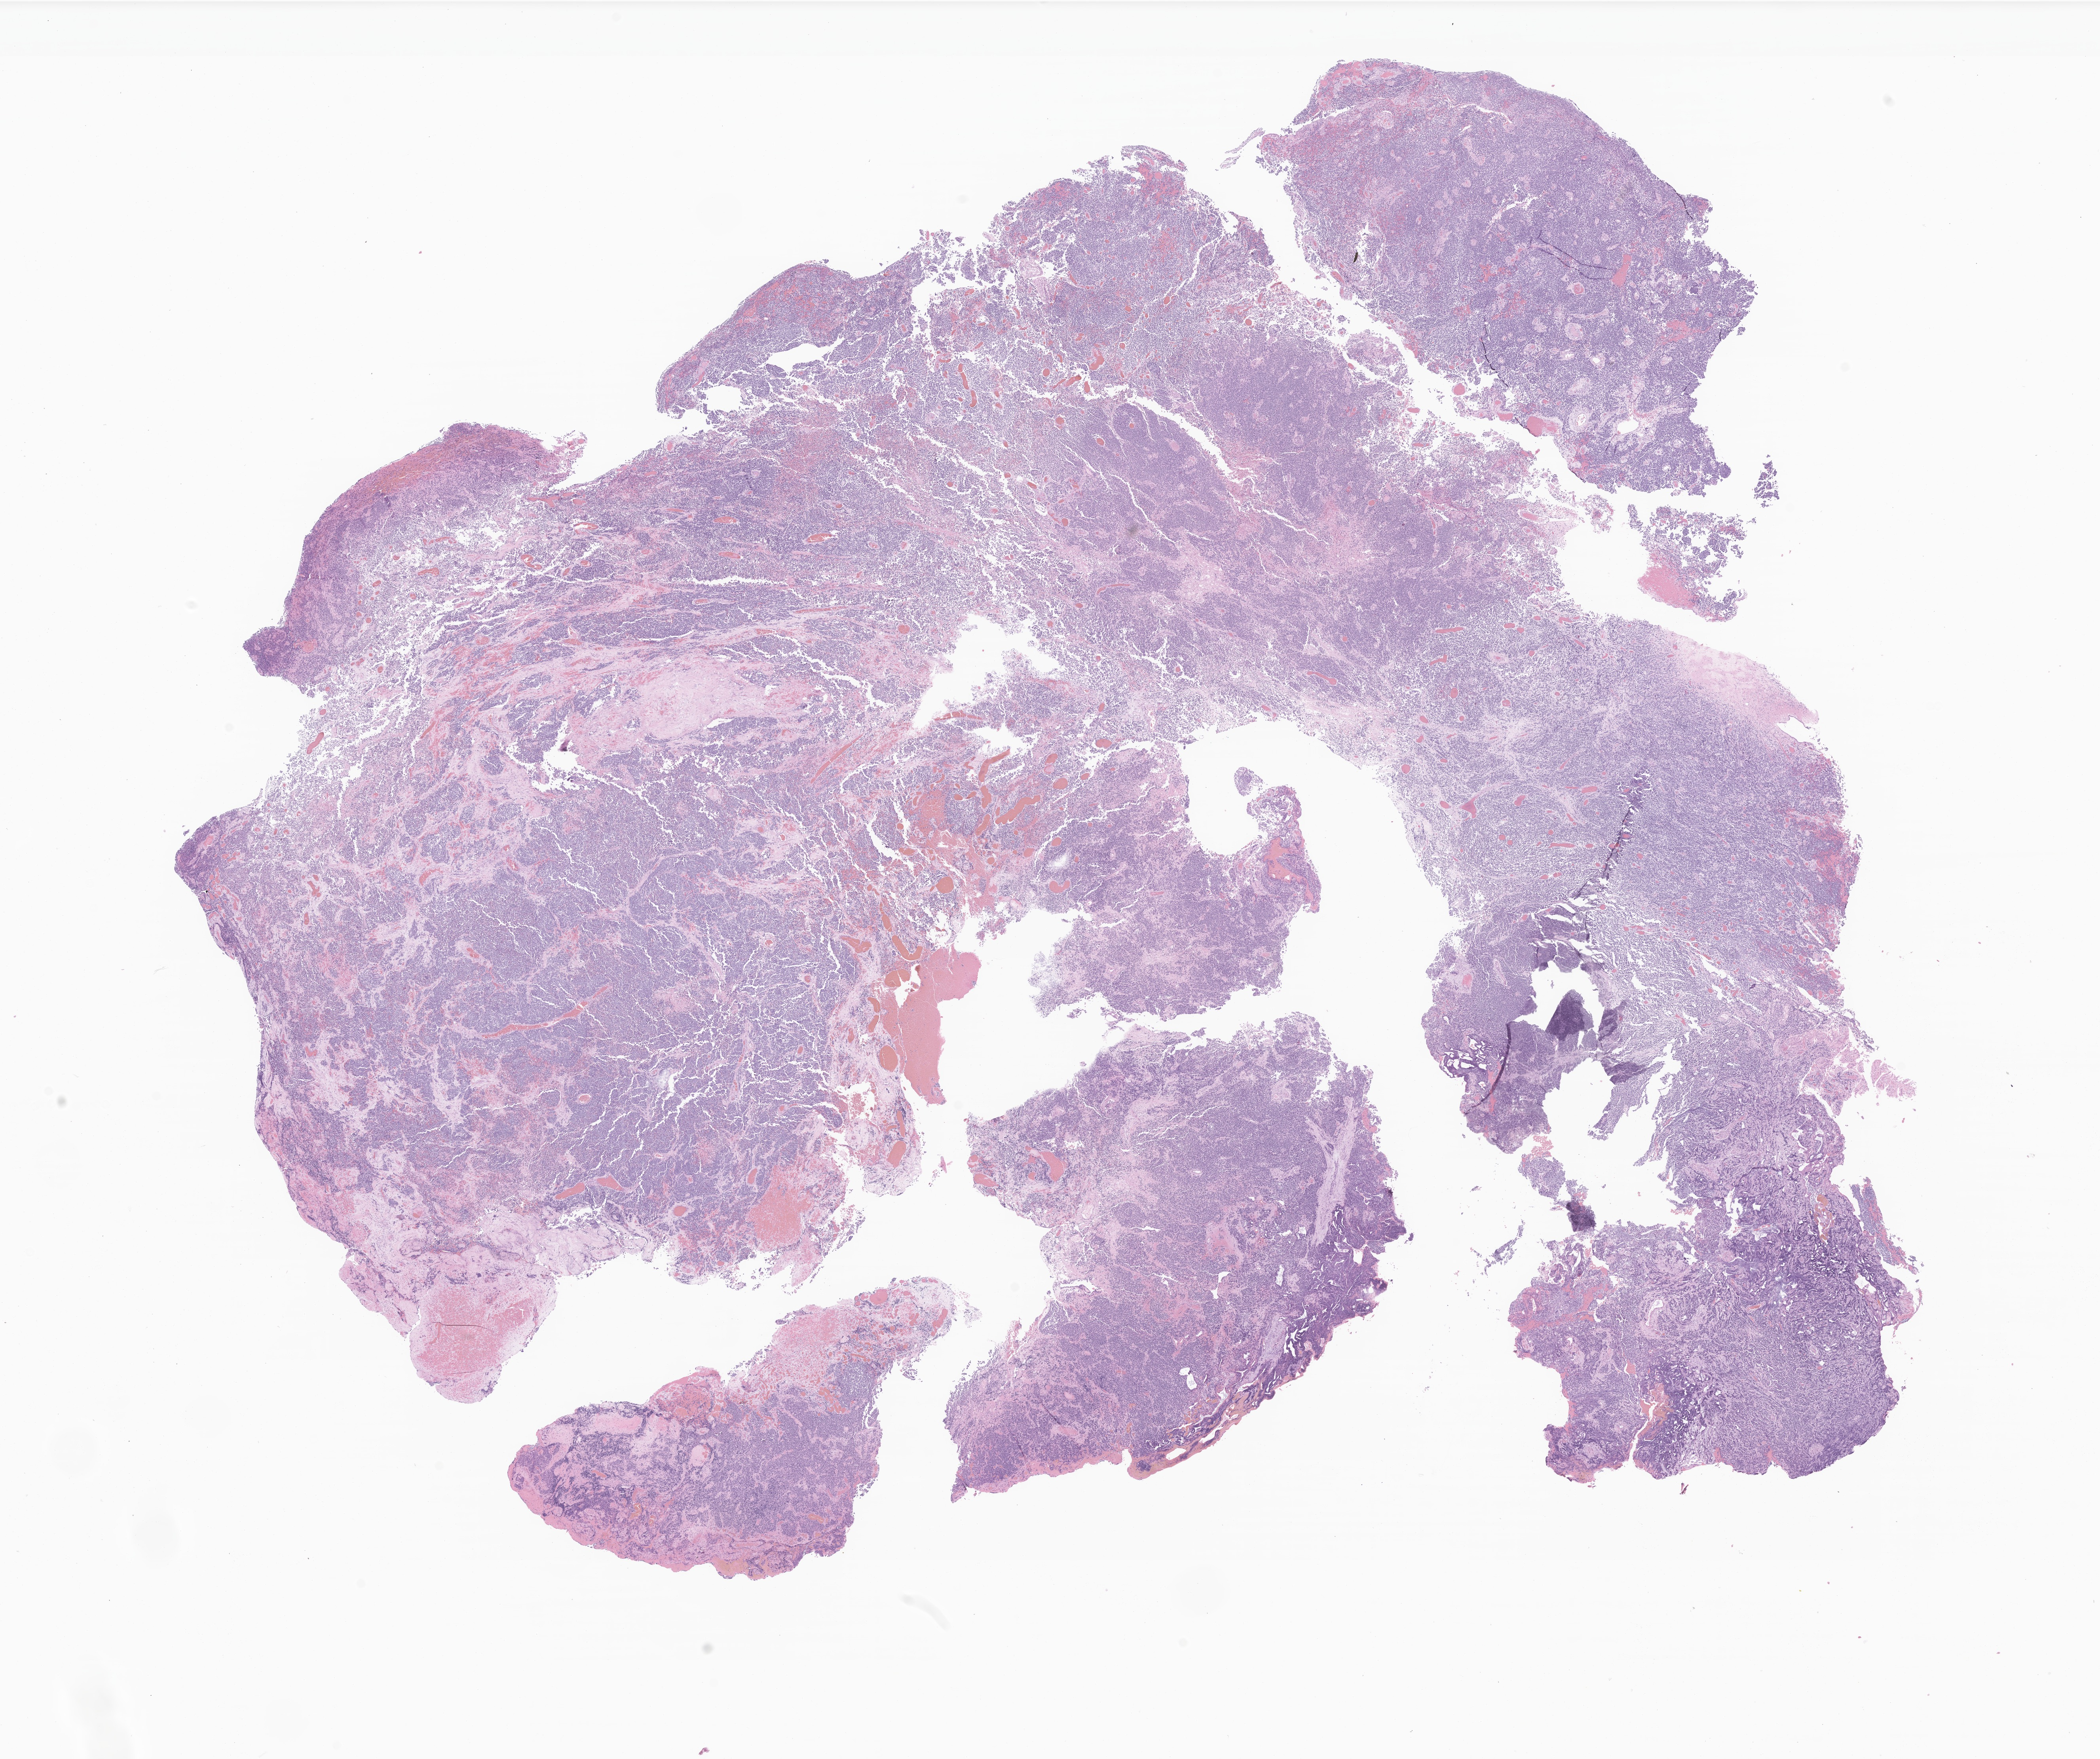
H&E whole-slide image of tumor tissue from the brain, whole scanned area (about 22.4 x 18.7 mm) shown as a low-resolution overview, formalin-fixed paraffin-embedded section. Patient male; age 52 months.
Diagnosis (ICD-O-3 morphology term): Medulloblastoma, NOS.